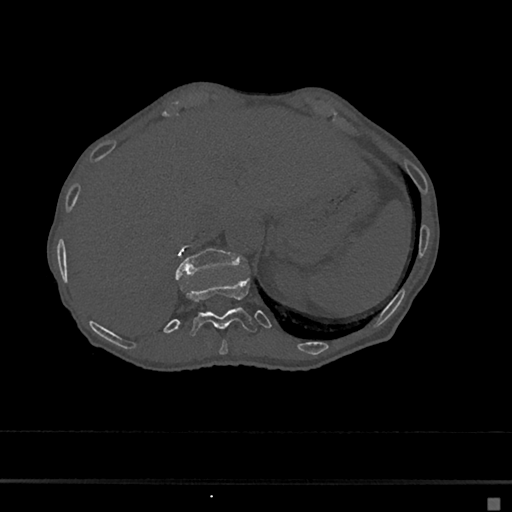
CT including the spine, one axial slice; position 170 of 797 along the scan axis; 120 kVp; bone window (W 1800 / L 400 HU); 512 × 512 image matrix, field of view 360 × 360 mm. Patient: female, 68 years. From the clinical record (not read from this slice): primary cancer: renal.
Annotated regions visible in this slice (semi-automatic segmentation, software-assisted and operator-edited):
- T10 vertebra: bounding box [x1, y1, x2, y2] px = [219, 339, 228, 355]
- T11 vertebra: [180, 277, 257, 337]
- T12 vertebra: [175, 247, 239, 279]